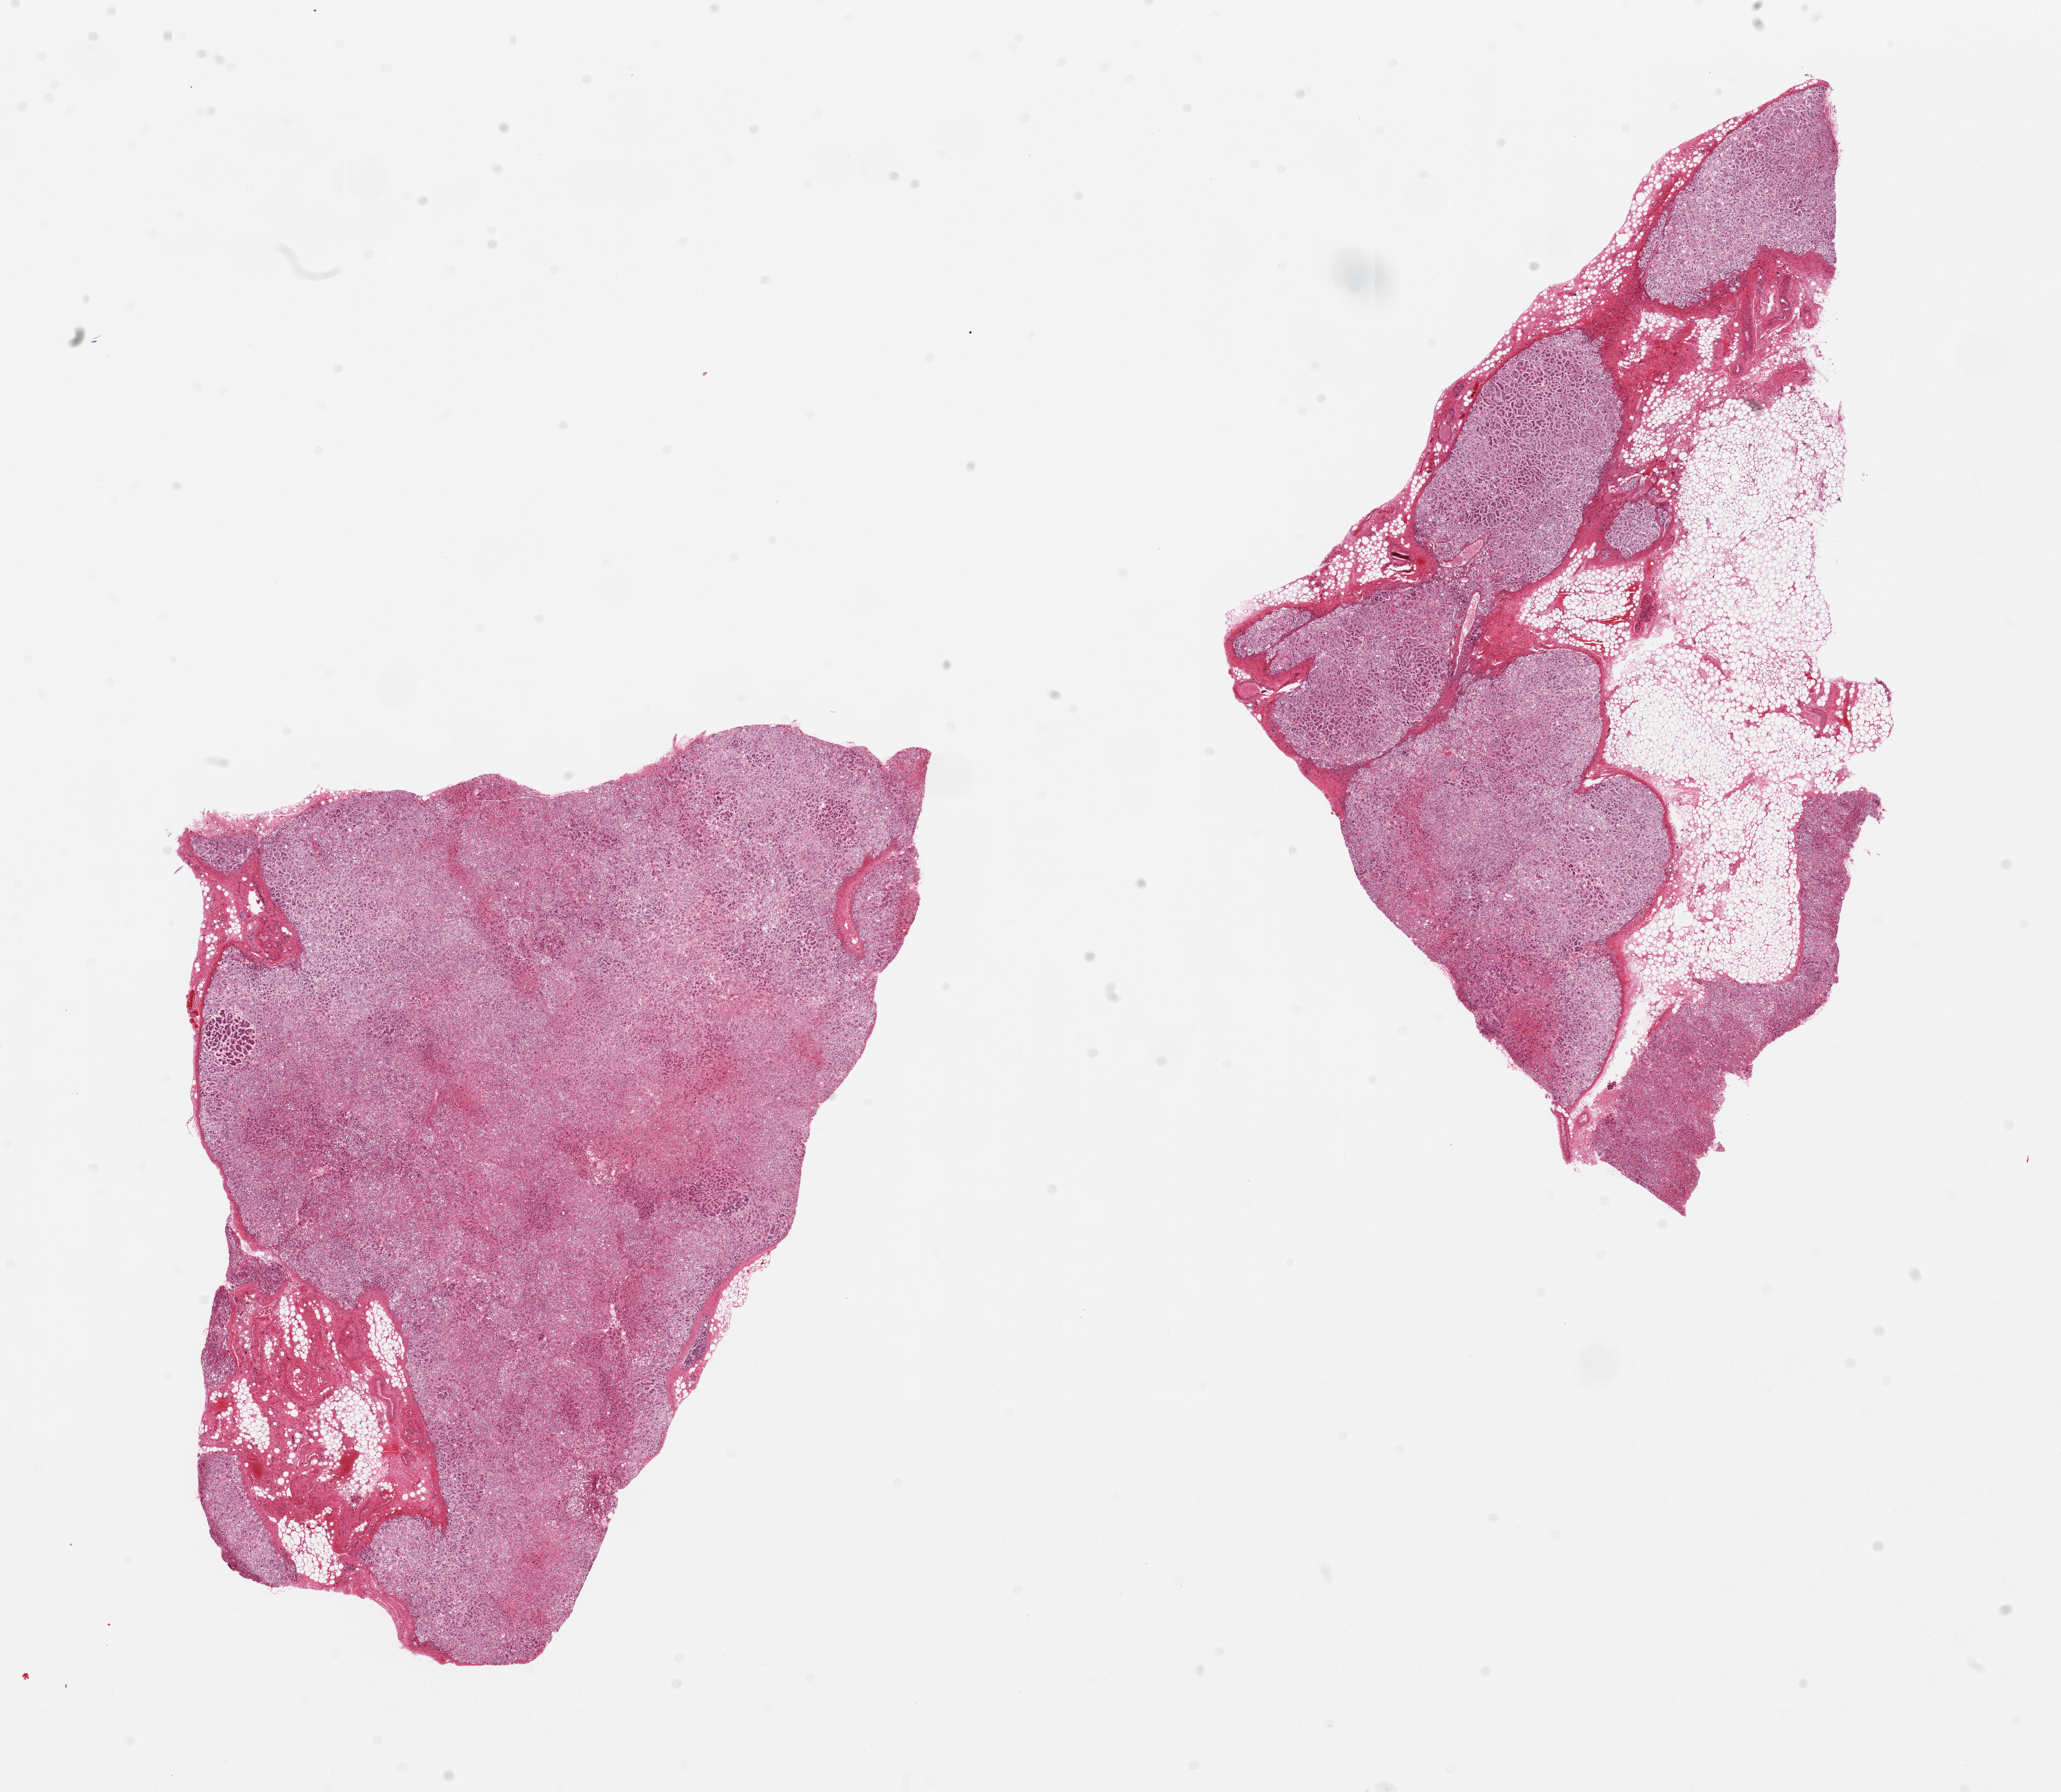
Haematoxylin and eosin whole-slide image — shown as a low-resolution overview of the whole scanned area (about 23.6 x 20.5 mm), PAXgene-fixed paraffin-embedded (PFPE) section, target tissue: adrenal gland, donor tissue sample. Donor: female.
Review note (as recorded): 2 pieces, 1 with 40% periadrenal fat.